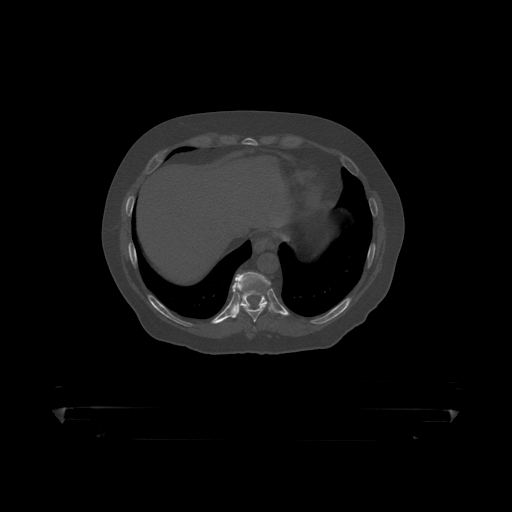
CT including the spine, one axial slice; position 228 of 390 along the scan axis; reconstruction kernel STANDARD; bone window (W 1800 / L 400 HU); 512 × 512 image matrix, field of view 650 × 650 mm. Male patient, age 60 years. Case-level facts recorded for this patient, not image findings: primary cancer: prostate.
Annotated regions visible in this slice (semi-automatically segmented with operator editing):
- T10 vertebra: bounding box <235,272,271,307> (left, top, right, bottom; pixels)
- T9 vertebra: <232,285,268,319>